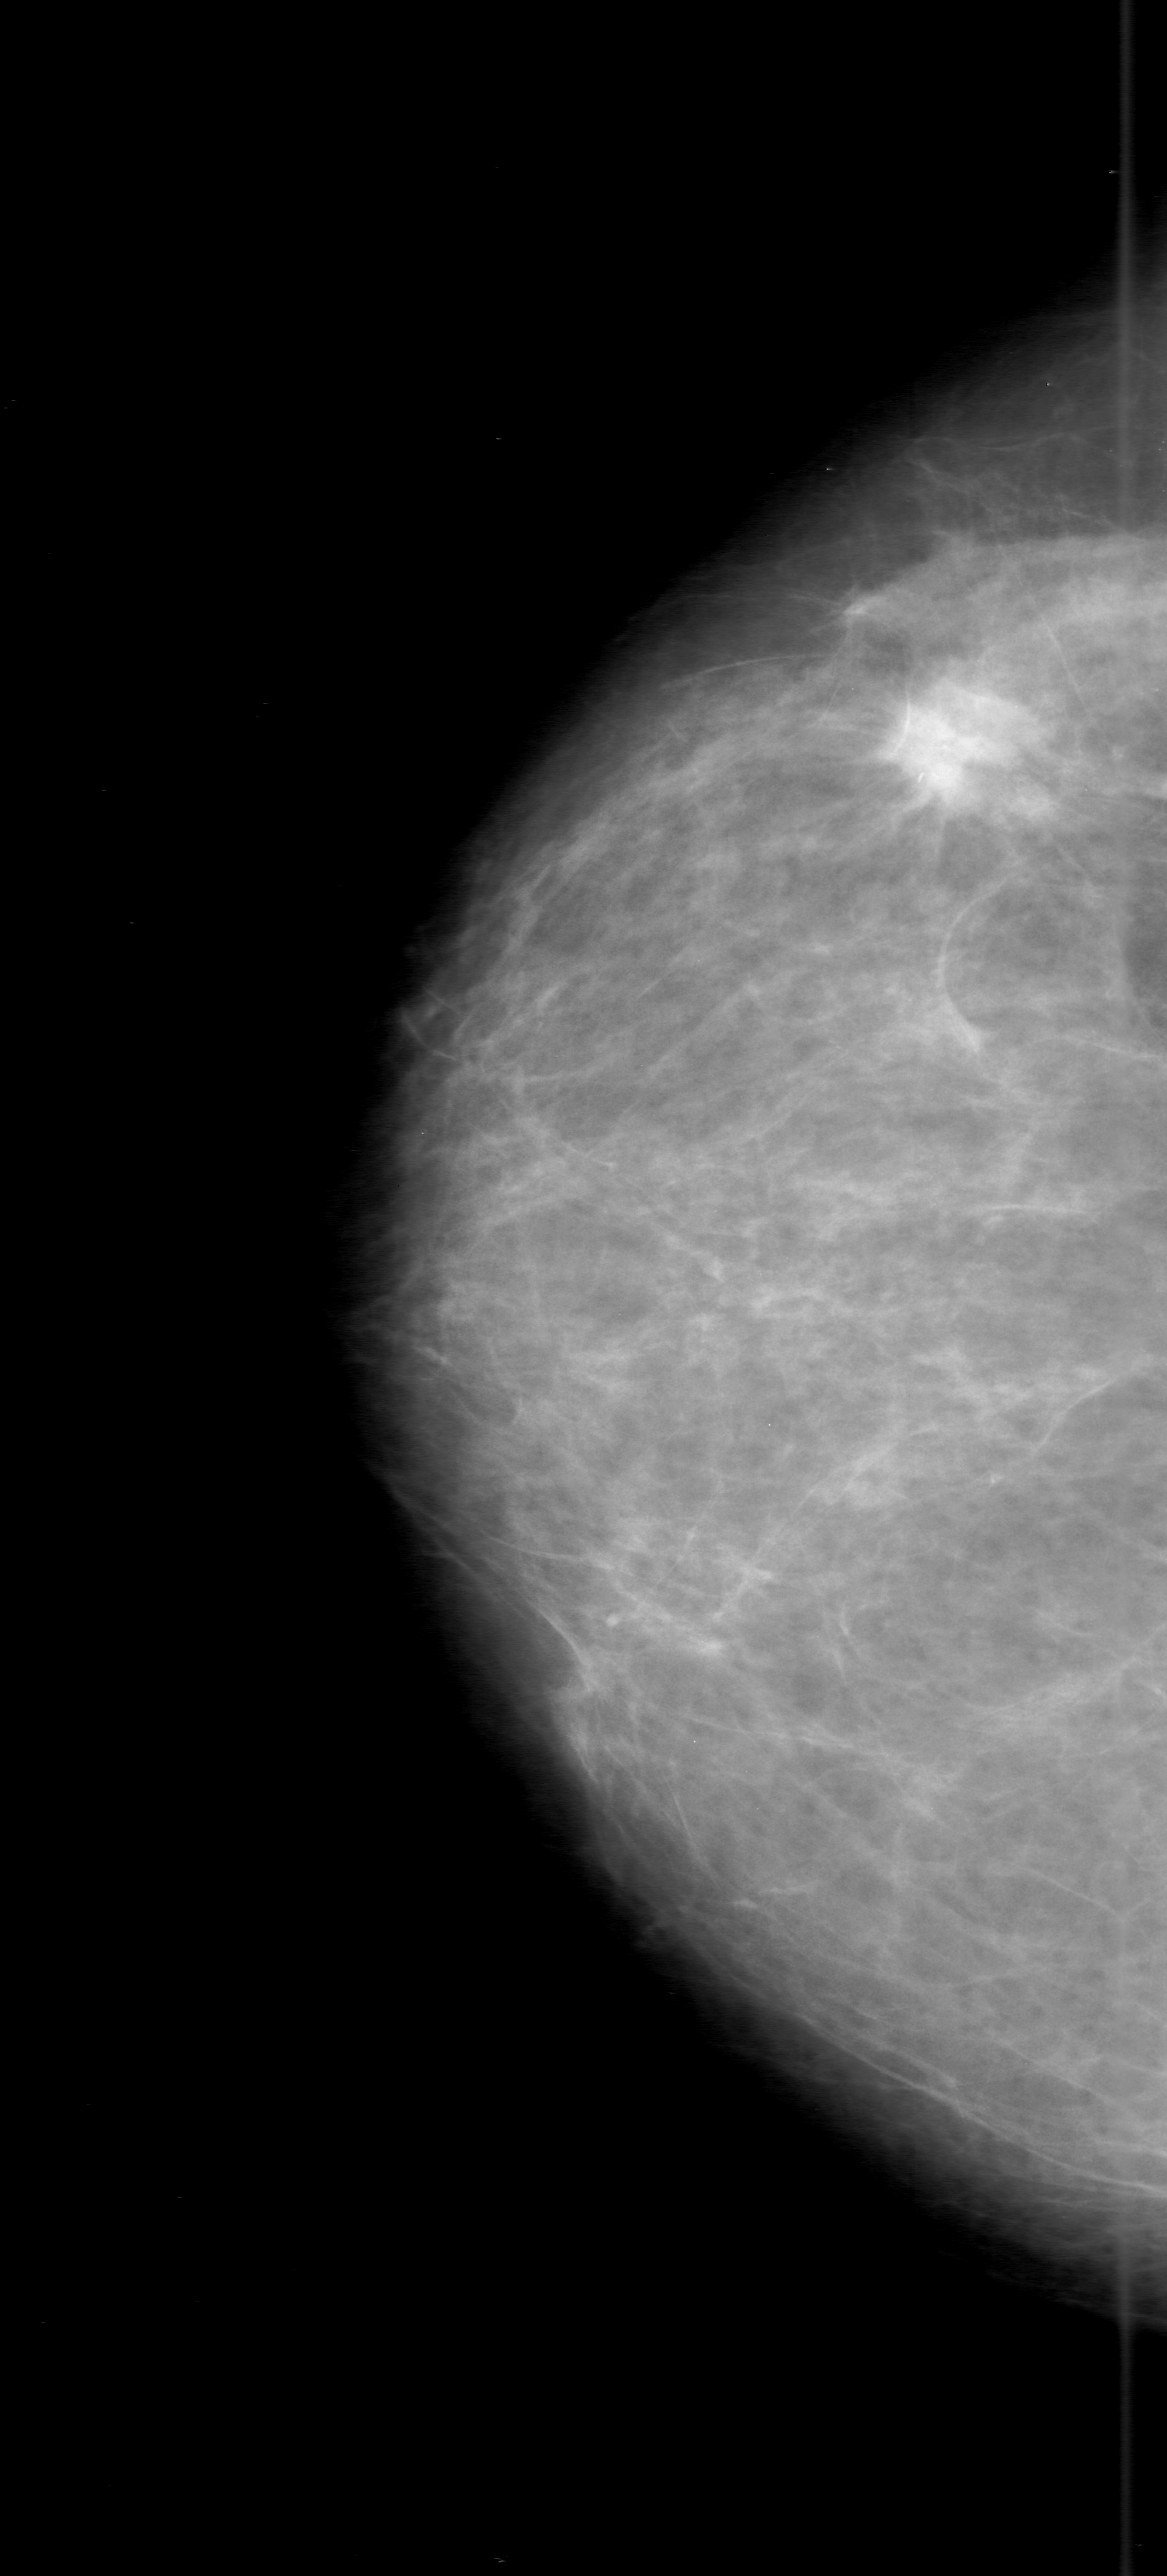
Mammogram (digitized film), right breast, CC view, breast composition: scattered fibroglandular densities (BI-RADS density category 2 of 4).
Mass, shape irregular, margins obscured; BI-RADS assessment category 3; pathology result (as recorded, not read from the image): malignant.